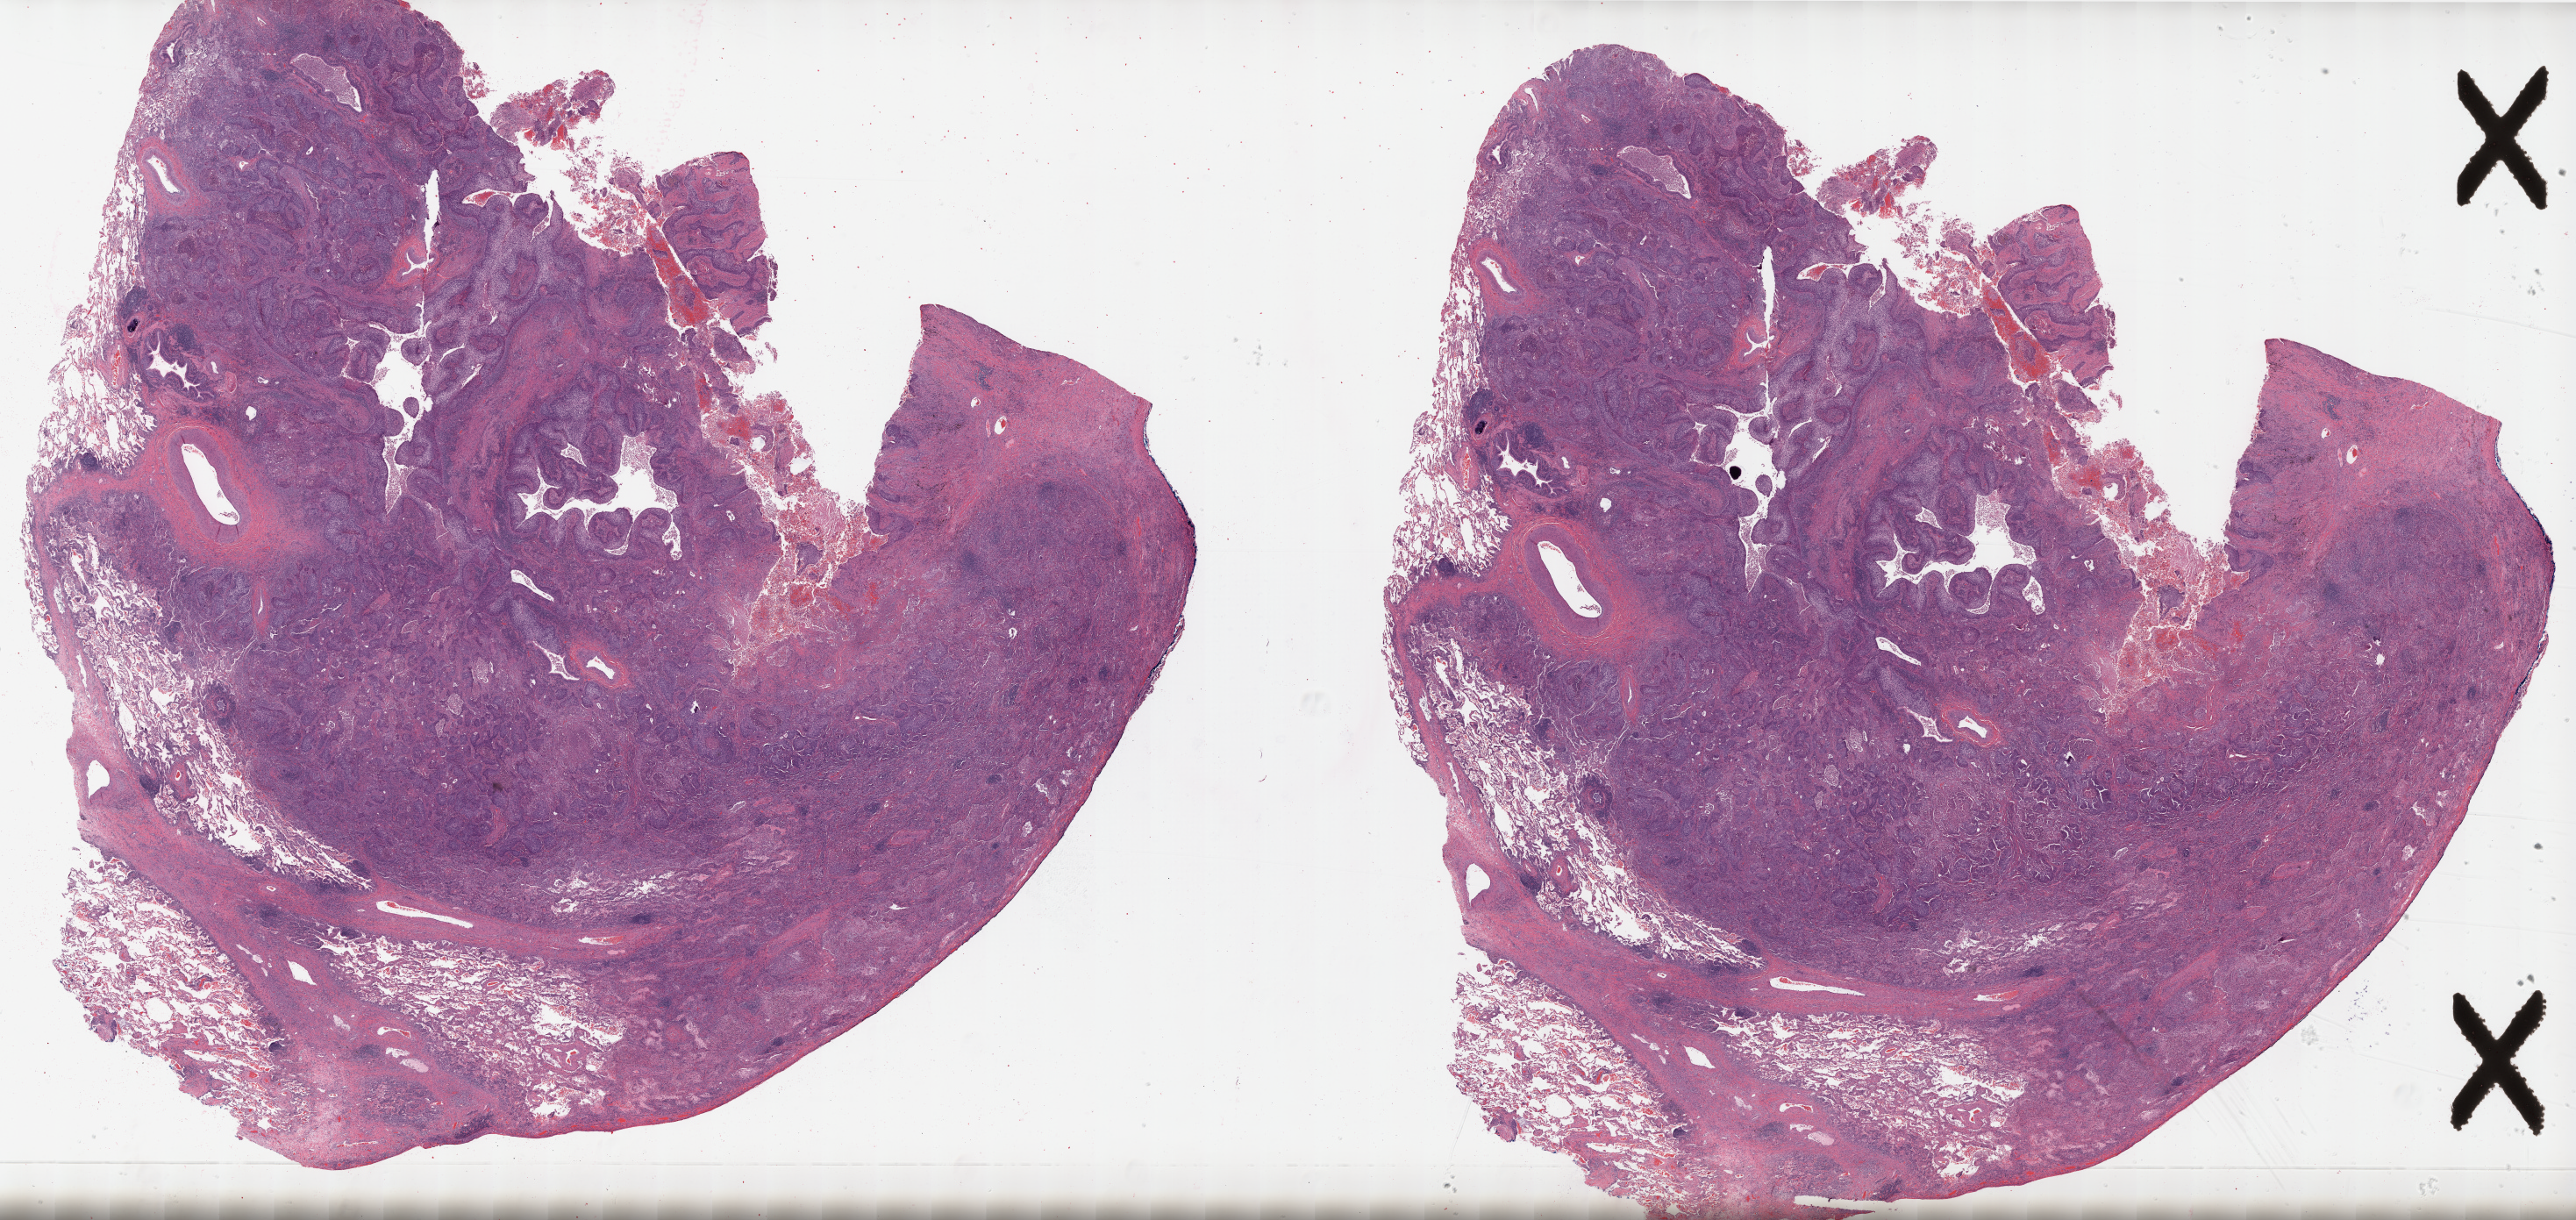
Whole-slide histology image, H&E, low-resolution overview of the scanned area, about 47.2 x 22.4 mm (acquisition: 20x scan). Formalin-fixed paraffin-embedded (FFPE) diagnostic section. Sample: primary tumour, lung. Male, age 73 years at initial diagnosis.
AJCC pathologic stage: IB. Histologic diagnosis: Squamous cell carcinoma, NOS (upper lobe, lung).